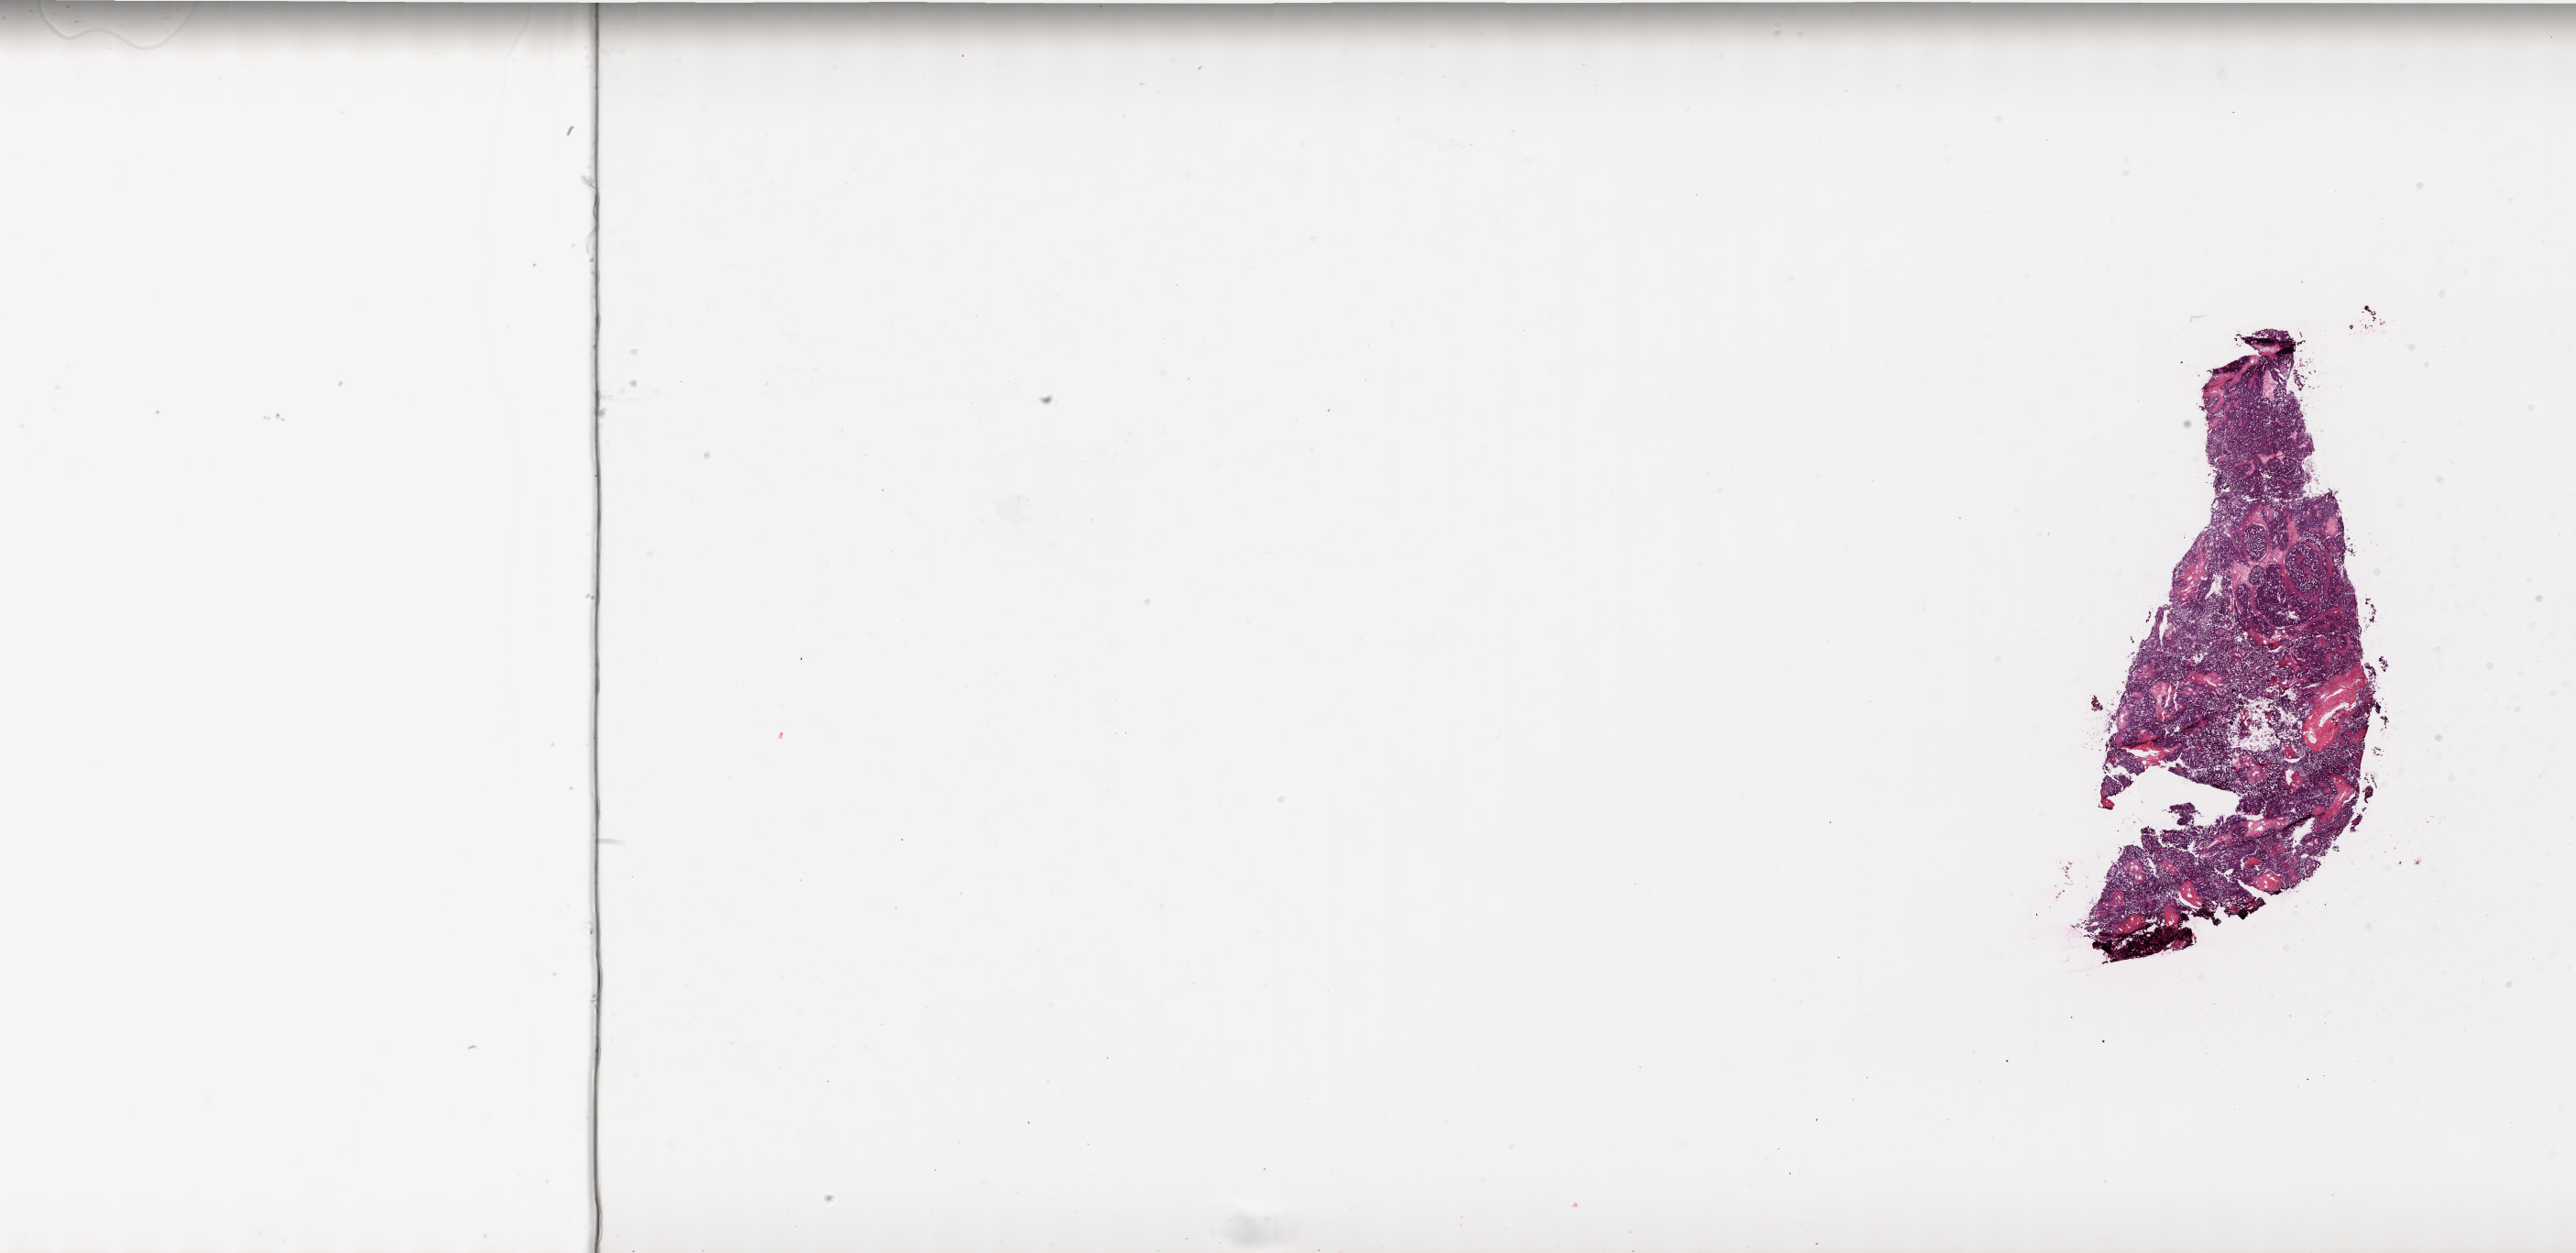
Whole-slide histology image, H&E, shown as a low-resolution overview of the whole scanned area (about 44.9 x 21.8 mm, acquisition: 20x scan), frozen section from the top of the tissue portion, primary tumour sample from the ovary. Female, age 59 years at initial diagnosis. Slide review estimates, as recorded: tumour cells 84%, tumour nuclei 99%.
Histologic diagnosis: Serous cystadenocarcinoma, NOS.